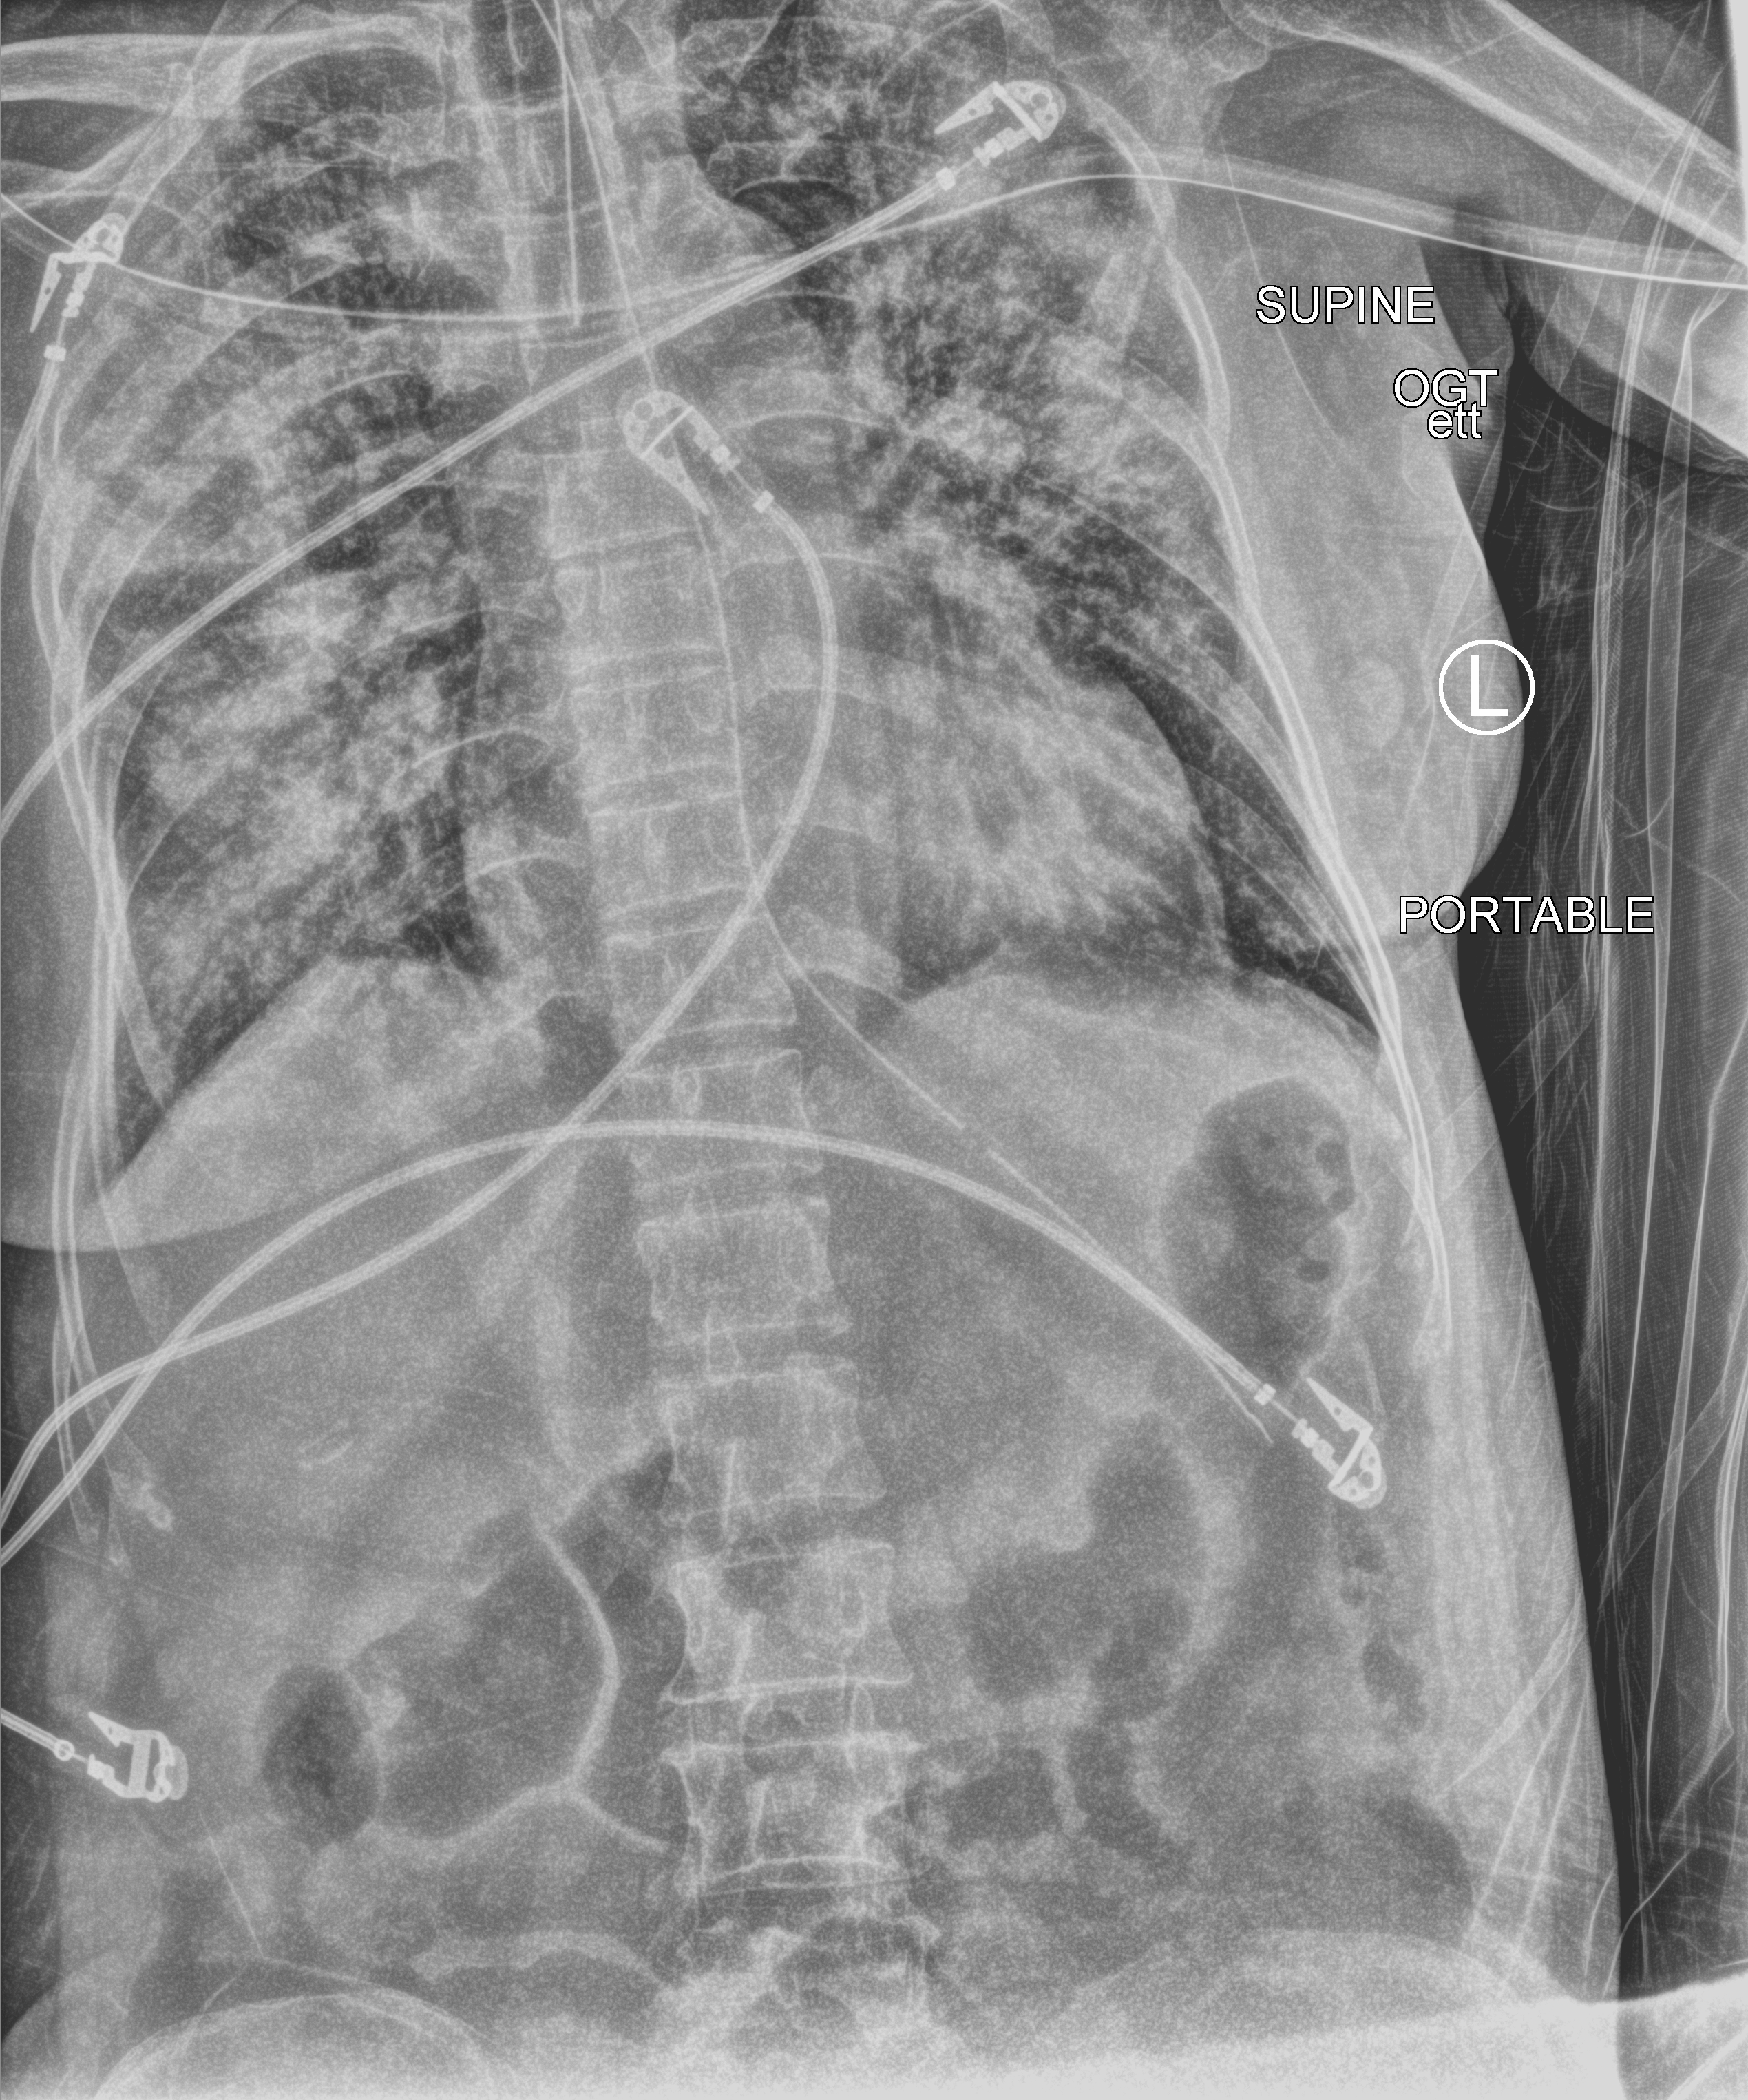
Portable chest radiograph; anteroposterior (AP) projection. Patient hospitalised with COVID-19; female, aged 60–74 years.
Admission-level facts for this patient (not findings on this image; timing relative to this image not recorded):
- admitted to intensive care during this hospital stay: yes
- other chronic lung disease (admission record): no
- COPD (admission record): no